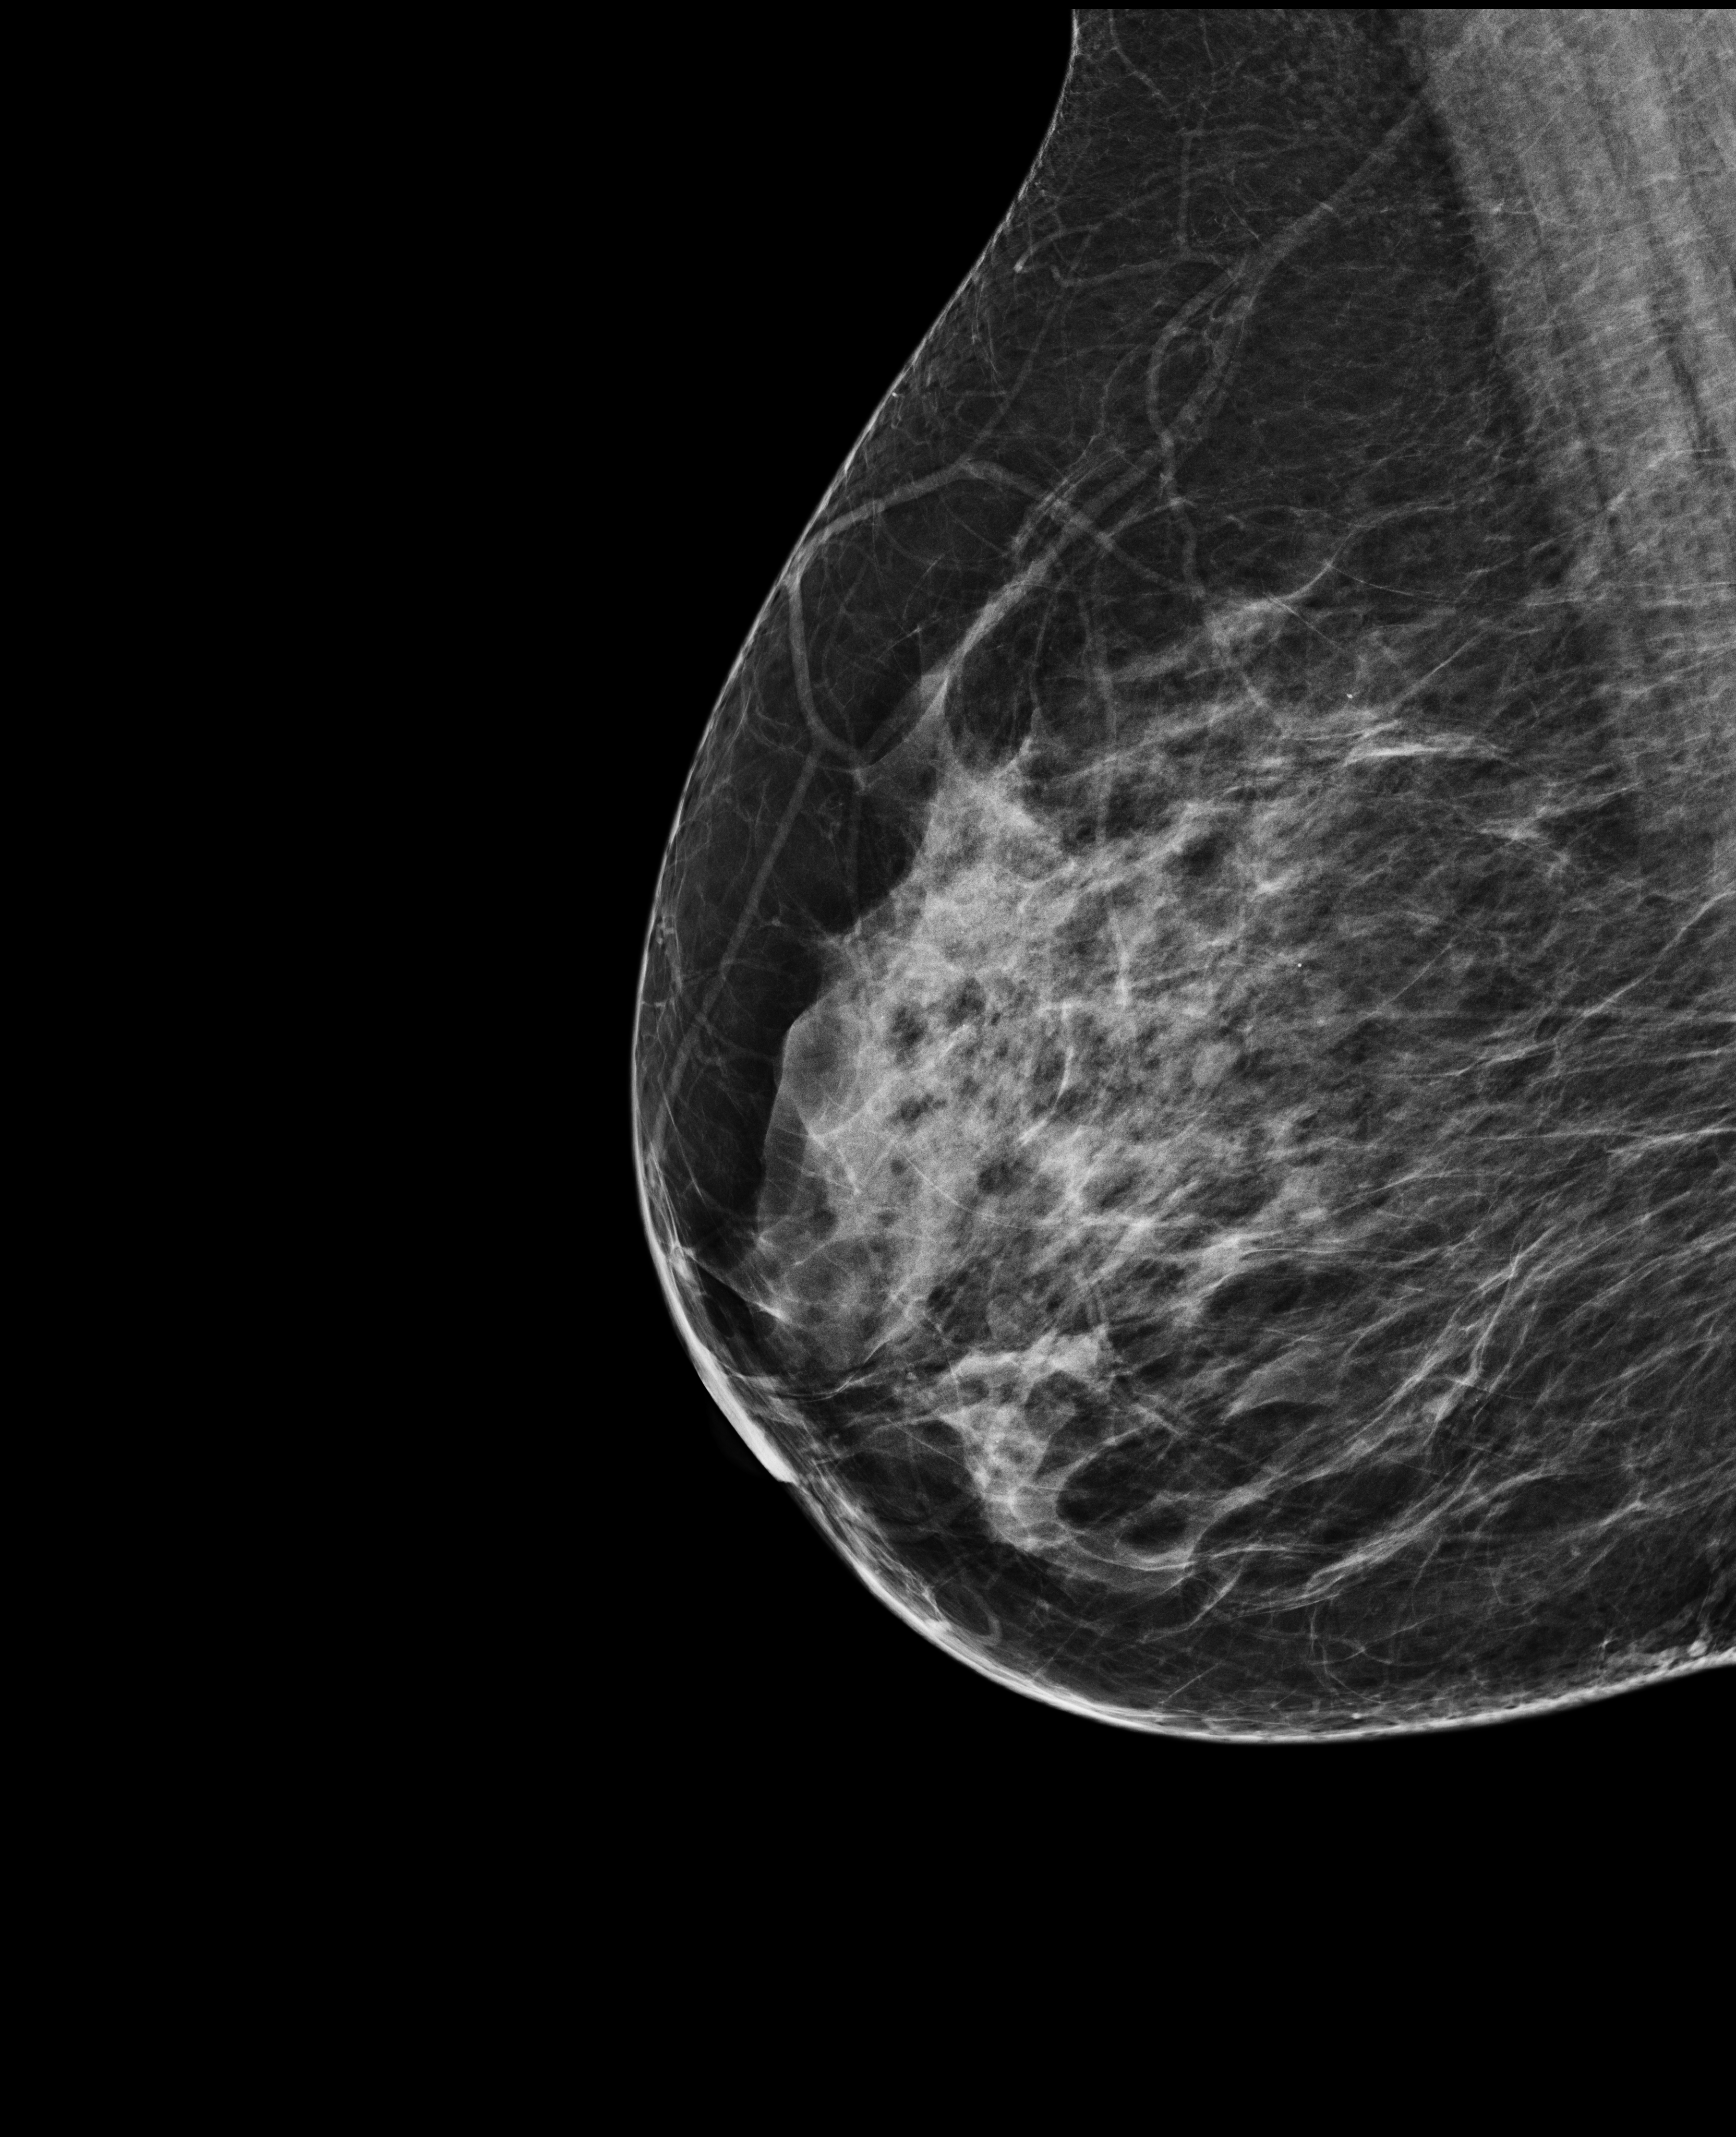
Annual screening mammography examination. Patient aged 49 years (female).
Image type: full-field digital mammogram. Breast: right. Projection: MLO view.